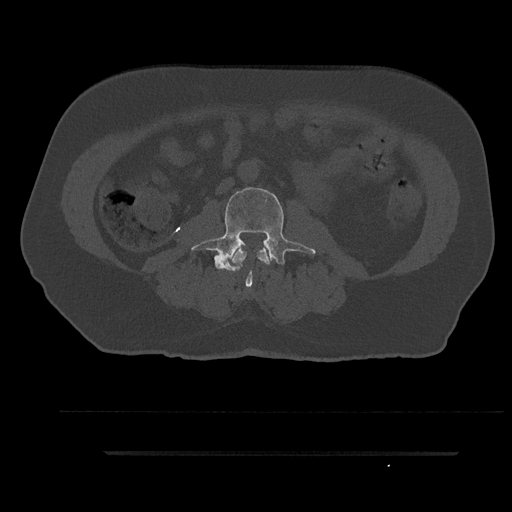
CT including the spine, one axial slice; position 56 of 797 along the scan axis; reconstruction kernel Br40s/3; bone window (W 1800 / L 400 HU); 512 × 512 image matrix, field of view 432 × 432 mm. Male patient, age 63 years. Case-level facts recorded for this patient, not image findings: primary cancer: renal; vertebrae with lytic lesions (as recorded): T8.
Outlined on this slice (semi-automatic segmentation, software-assisted and operator-edited):
- L2 vertebra: bounding box (x1, y1, x2, y2) in pixels: (232, 248, 270, 272)
- L3 vertebra: (191, 185, 316, 287)